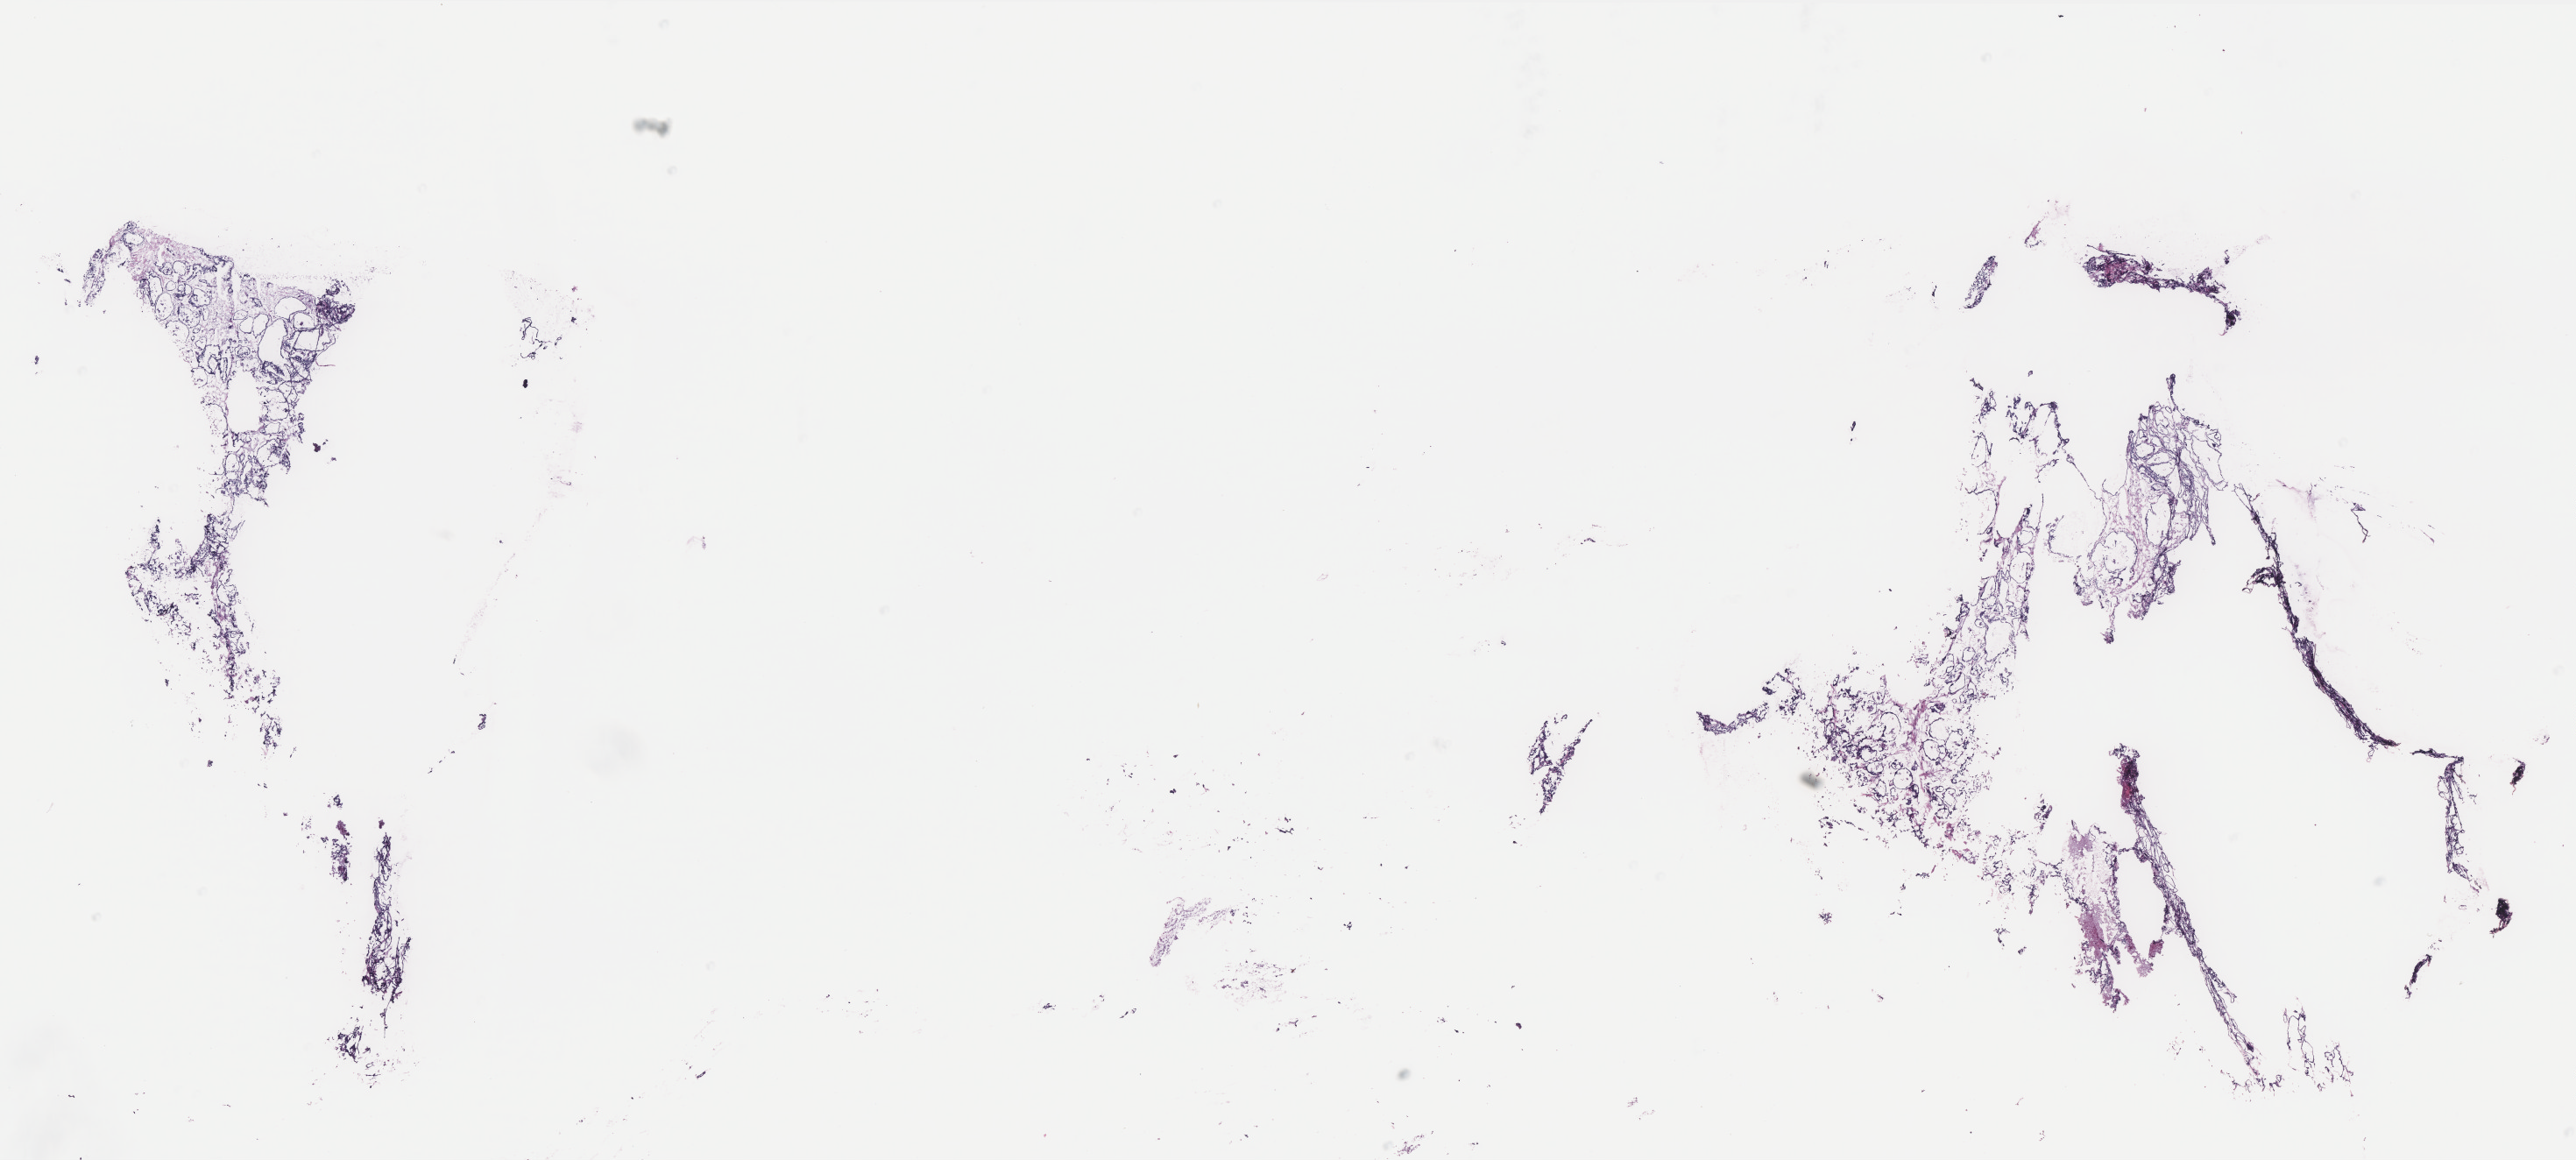
H&E-stained whole-slide image — low-resolution overview of the scanned area, about 23.6 x 10.6 mm. Frozen section from the top of the tissue portion. Primary tumour sample from the thyroid. Male patient; age at initial diagnosis 80 years. Pathologist review of this section (percent, as recorded): tumour cells 95%, tumour nuclei 99%, normal cells 0%, stromal cells 5%, necrosis 0%. Inflammatory infiltration, as recorded: lymphocyte infiltration 0%, monocyte infiltration 0%, neutrophil infiltration 0%.
• pathologic diagnosis: Papillary carcinoma, follicular variant (thyroid gland)
• AJCC pathologic stage: I